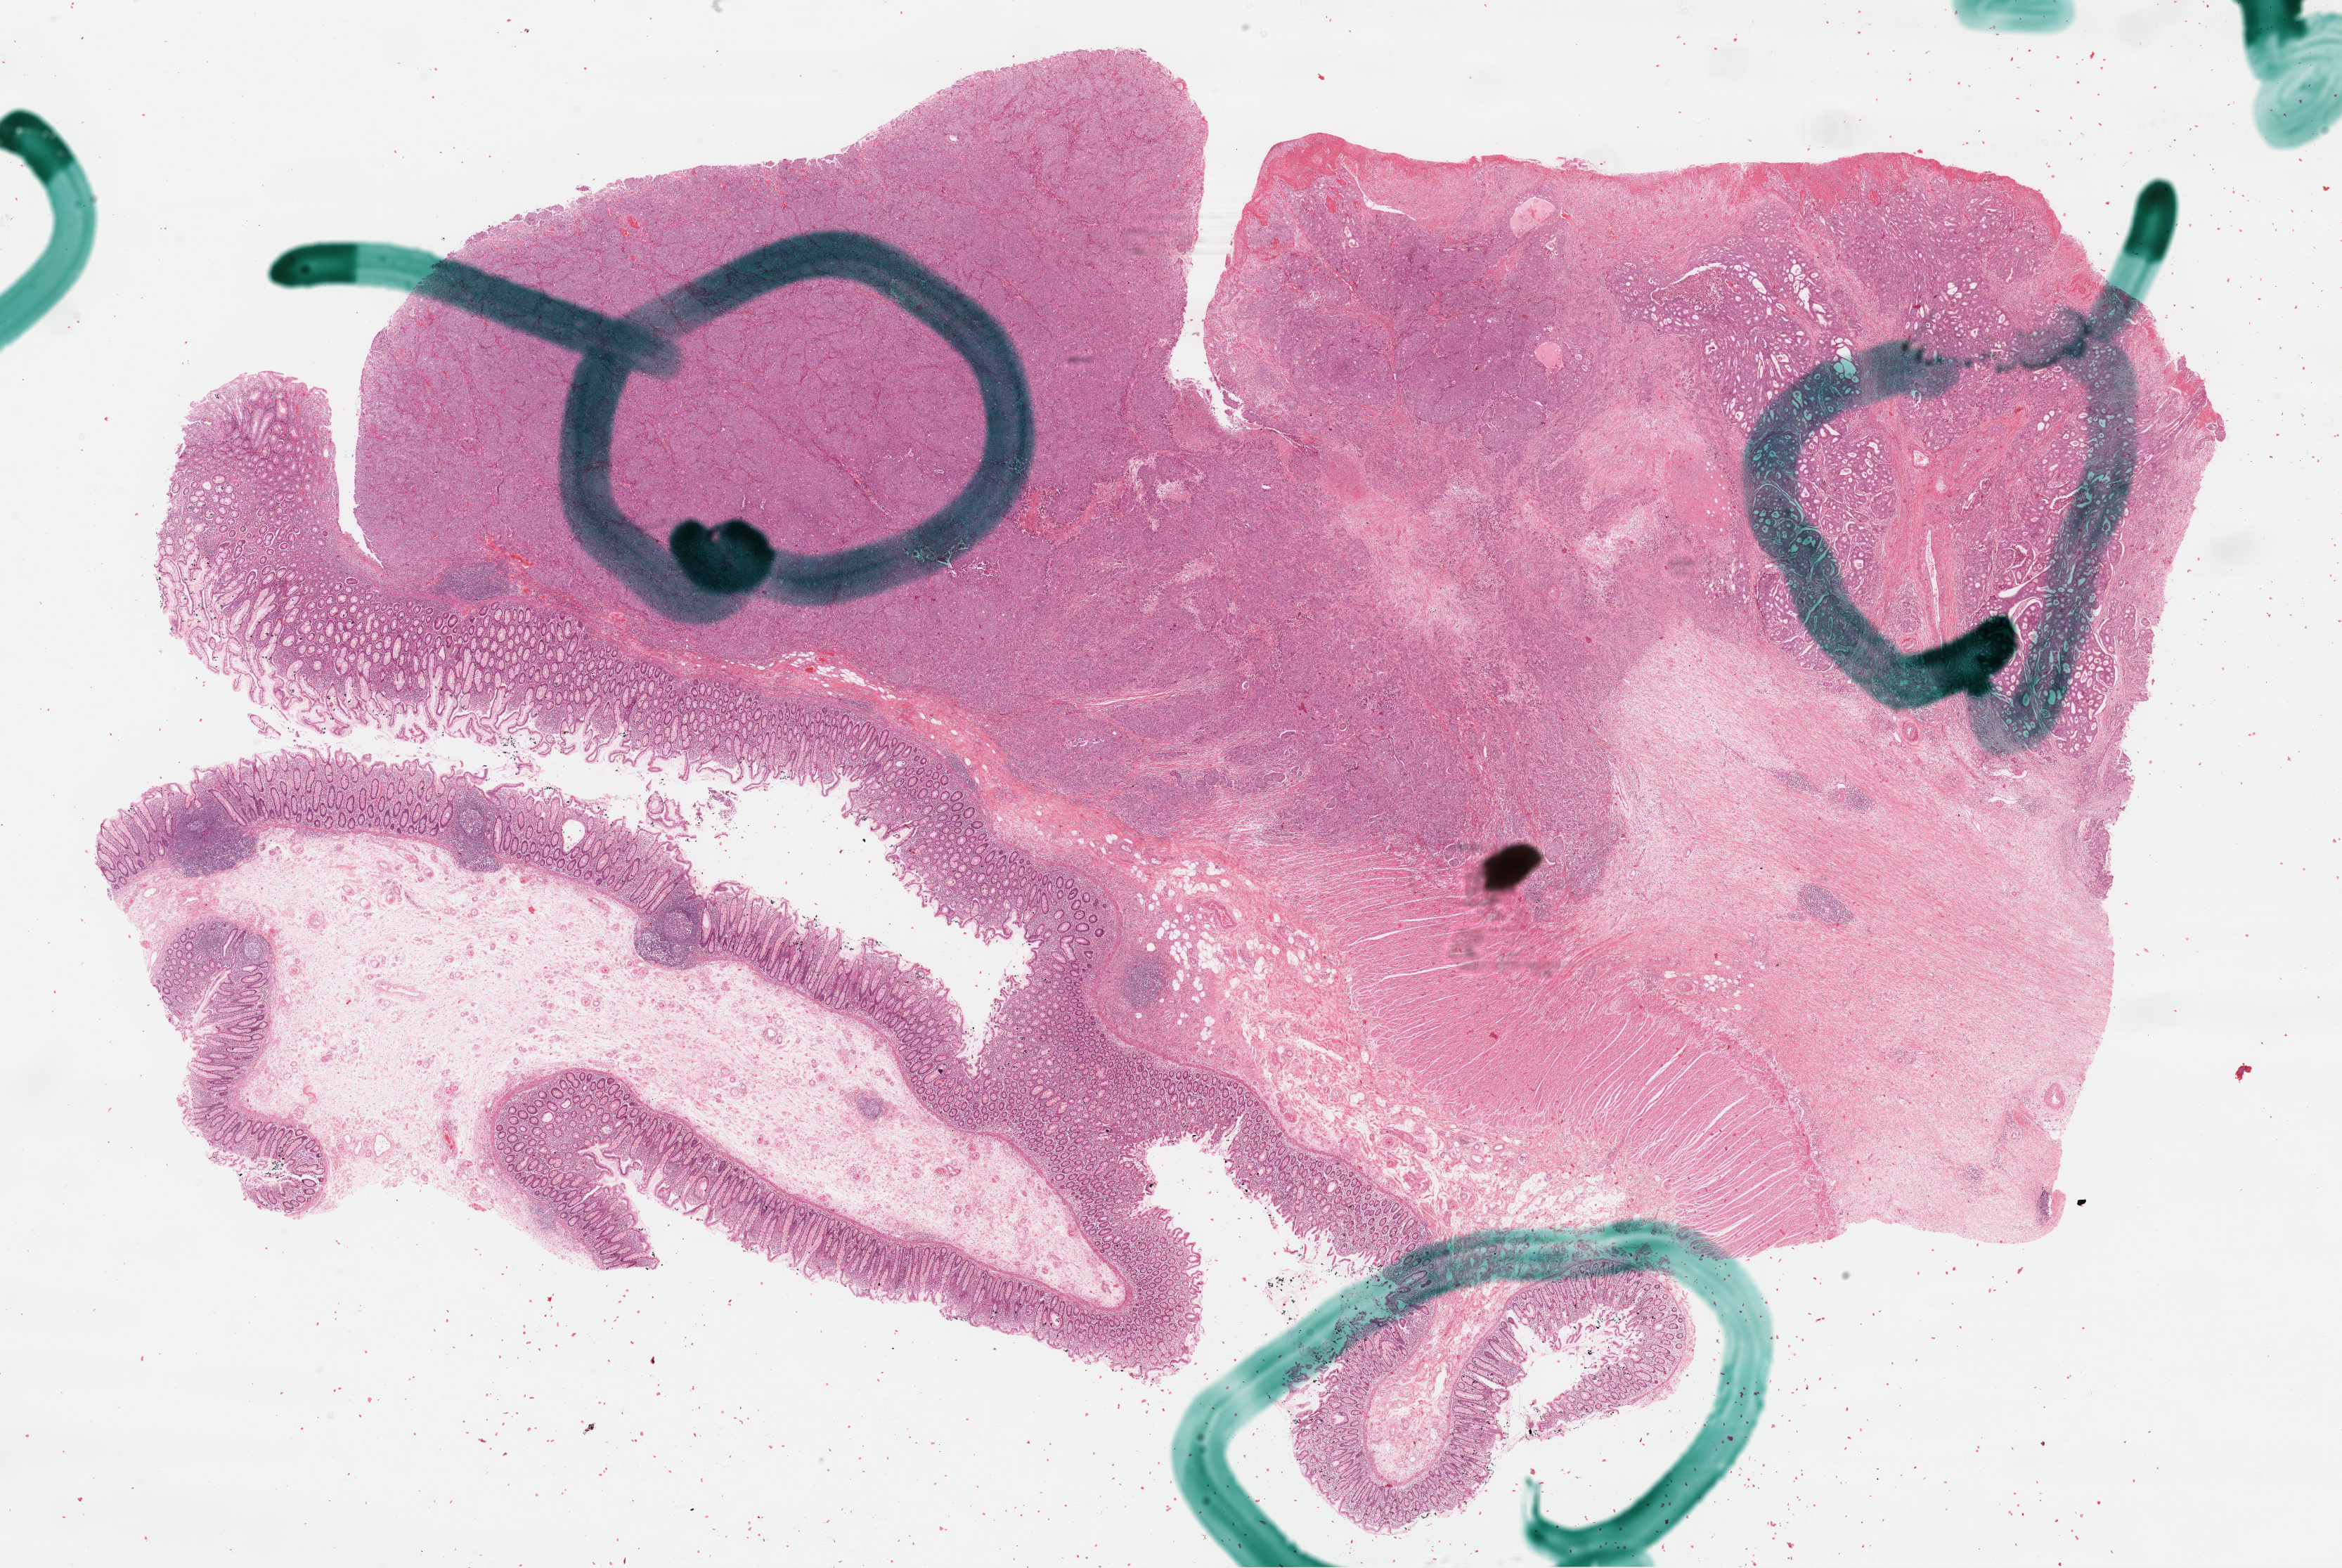
Hematoxylin and eosin (H&E) stained whole-slide image — a low-resolution overview of the entire scanned area, about 26.3 x 17.6 mm, formalin-fixed paraffin-embedded (FFPE) diagnostic section, sample: primary tumour, colon. Male patient.
Pathologic diagnosis: Adenocarcinoma, NOS (ascending colon). AJCC pathologic stage: IIIC. Lymph nodes positive (case pathology): 4 of 17 examined.